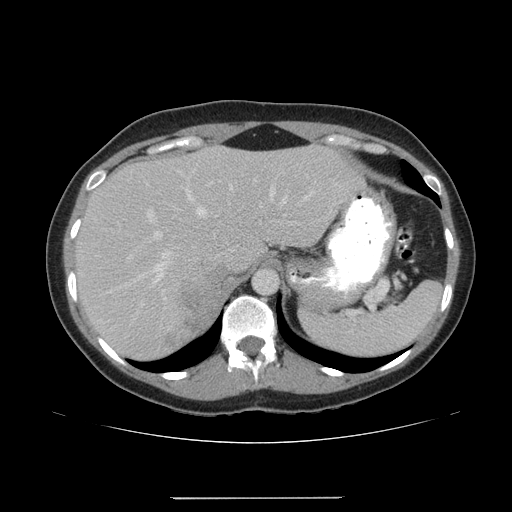
Contrast-enhanced abdominal CT, one axial slice. Position 127 of 161 along the scan axis. Reconstruction kernel STANDARD. 120 kVp. Intravenous contrast given. Soft-tissue window (W 400 / L 40 HU). 3.75 mm slice thickness. 512 × 512 image matrix, field of view 380 × 380 mm. Female patient. Case-level facts recorded for this patient, not image findings: diagnosis: adrenocortical carcinoma; tumour side: right adrenal; tumour size at pathology: 9 cm; Ki-67 index: 14 %; stage (as recorded): 3.
Annotated regions visible in this slice (semi-automatic segmentation, software-assisted and operator-edited):
- mass: box from (x=180, y=266) to (x=234, y=329) px